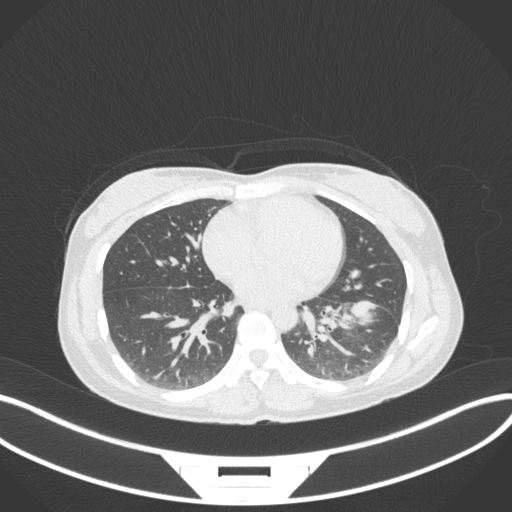
Chest CT, one axial slice. Position 151 of 361 along the scan axis. Reconstruction kernel B31f. Lung window (W 1500 / L -600 HU). 1 mm slice thickness. 512 × 512 image matrix, field of view 400 × 400 mm. Patient: female, 41 years. From the clinical record (not read from this slice): clinical TNM (as recorded): T2a N3 M1b.
Structures marked on this image (rectangle marked by the reading radiologist):
- lung tumour (recorded histology: adenocarcinoma): box from (x=350, y=297) to (x=386, y=333) px